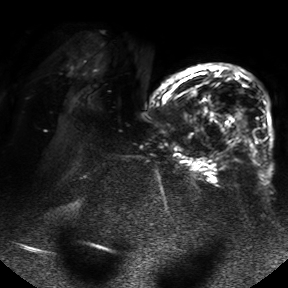
Breast MRI, one axial slice; slice 22 of 50 in the series (ordered by position); diffusion-weighted series; image 2 of 4 stored at this slice position (different b-values; order by instance number); 1.5 T; 4 mm slice thickness; 288 × 288 image matrix. Female patient.
Annotated regions visible in this slice (manually delineated by an expert):
- tumour on diffusion-weighted imaging: bounding box <236,115,246,130> (left, top, right, bottom; pixels)